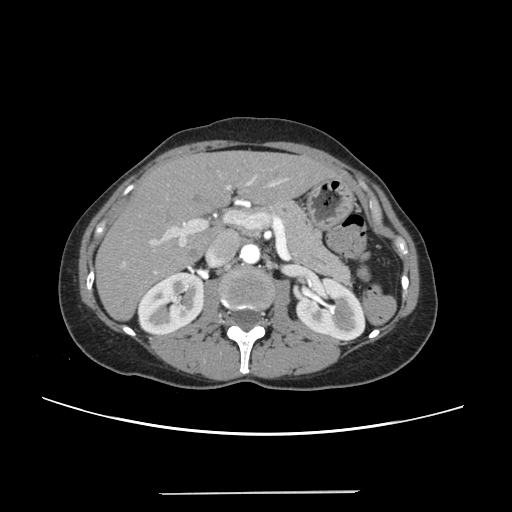
Contrast-enhanced abdominal CT, one axial slice; position 130 of 240 along the scan axis; intravenous contrast given; soft-tissue window (W 400 / L 40 HU); 512 × 512 image matrix. Female patient, age 60 years. Case-level facts recorded for this patient, not image findings: diagnosis: colorectal cancer liver metastases, imaged before liver resection.
Outlined on this slice (manually delineated by an expert):
- liver: bounding box (x1, y1, x2, y2) in pixels: (98, 152, 334, 319)
- planned liver remnant (the part of the liver to remain after resection): (98, 152, 333, 319)
- portal vein (with intrahepatic branches): (123, 176, 289, 274)
- liver metastasis: (206, 166, 210, 170)